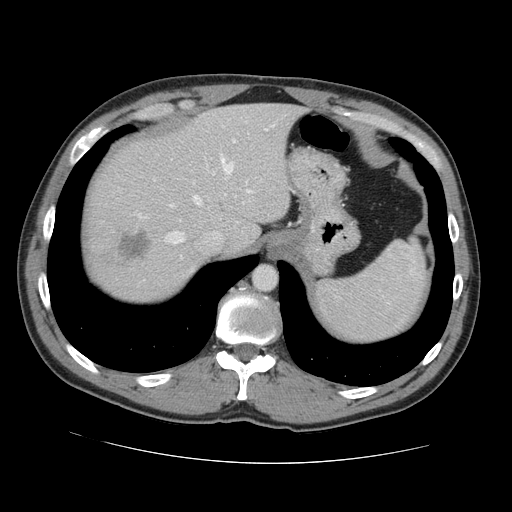
Contrast-enhanced abdominal CT, one axial slice; slice 111 of 131 in the series (ordered by position); intravenous contrast given; soft-tissue window (W 400 / L 40 HU); 512 × 512 image matrix, field of view 380 × 380 mm. Male patient, age 40 years. From the clinical record (not read from this slice): diagnosis: colorectal cancer liver metastases, imaged before liver resection; multiple liver metastases: yes; largest metastasis: 2.9 cm.
Annotated regions visible in this slice (outlined manually by an expert reader):
- hepatic veins: box from (x=165, y=157) to (x=233, y=244) px
- liver: (x=84, y=104)–(x=301, y=300)
- planned liver remnant (the part of the liver to remain after resection): (x=107, y=104)–(x=301, y=252)
- portal vein (with intrahepatic branches): (x=214, y=133)–(x=253, y=193)
- liver metastasis: (x=116, y=229)–(x=150, y=262)